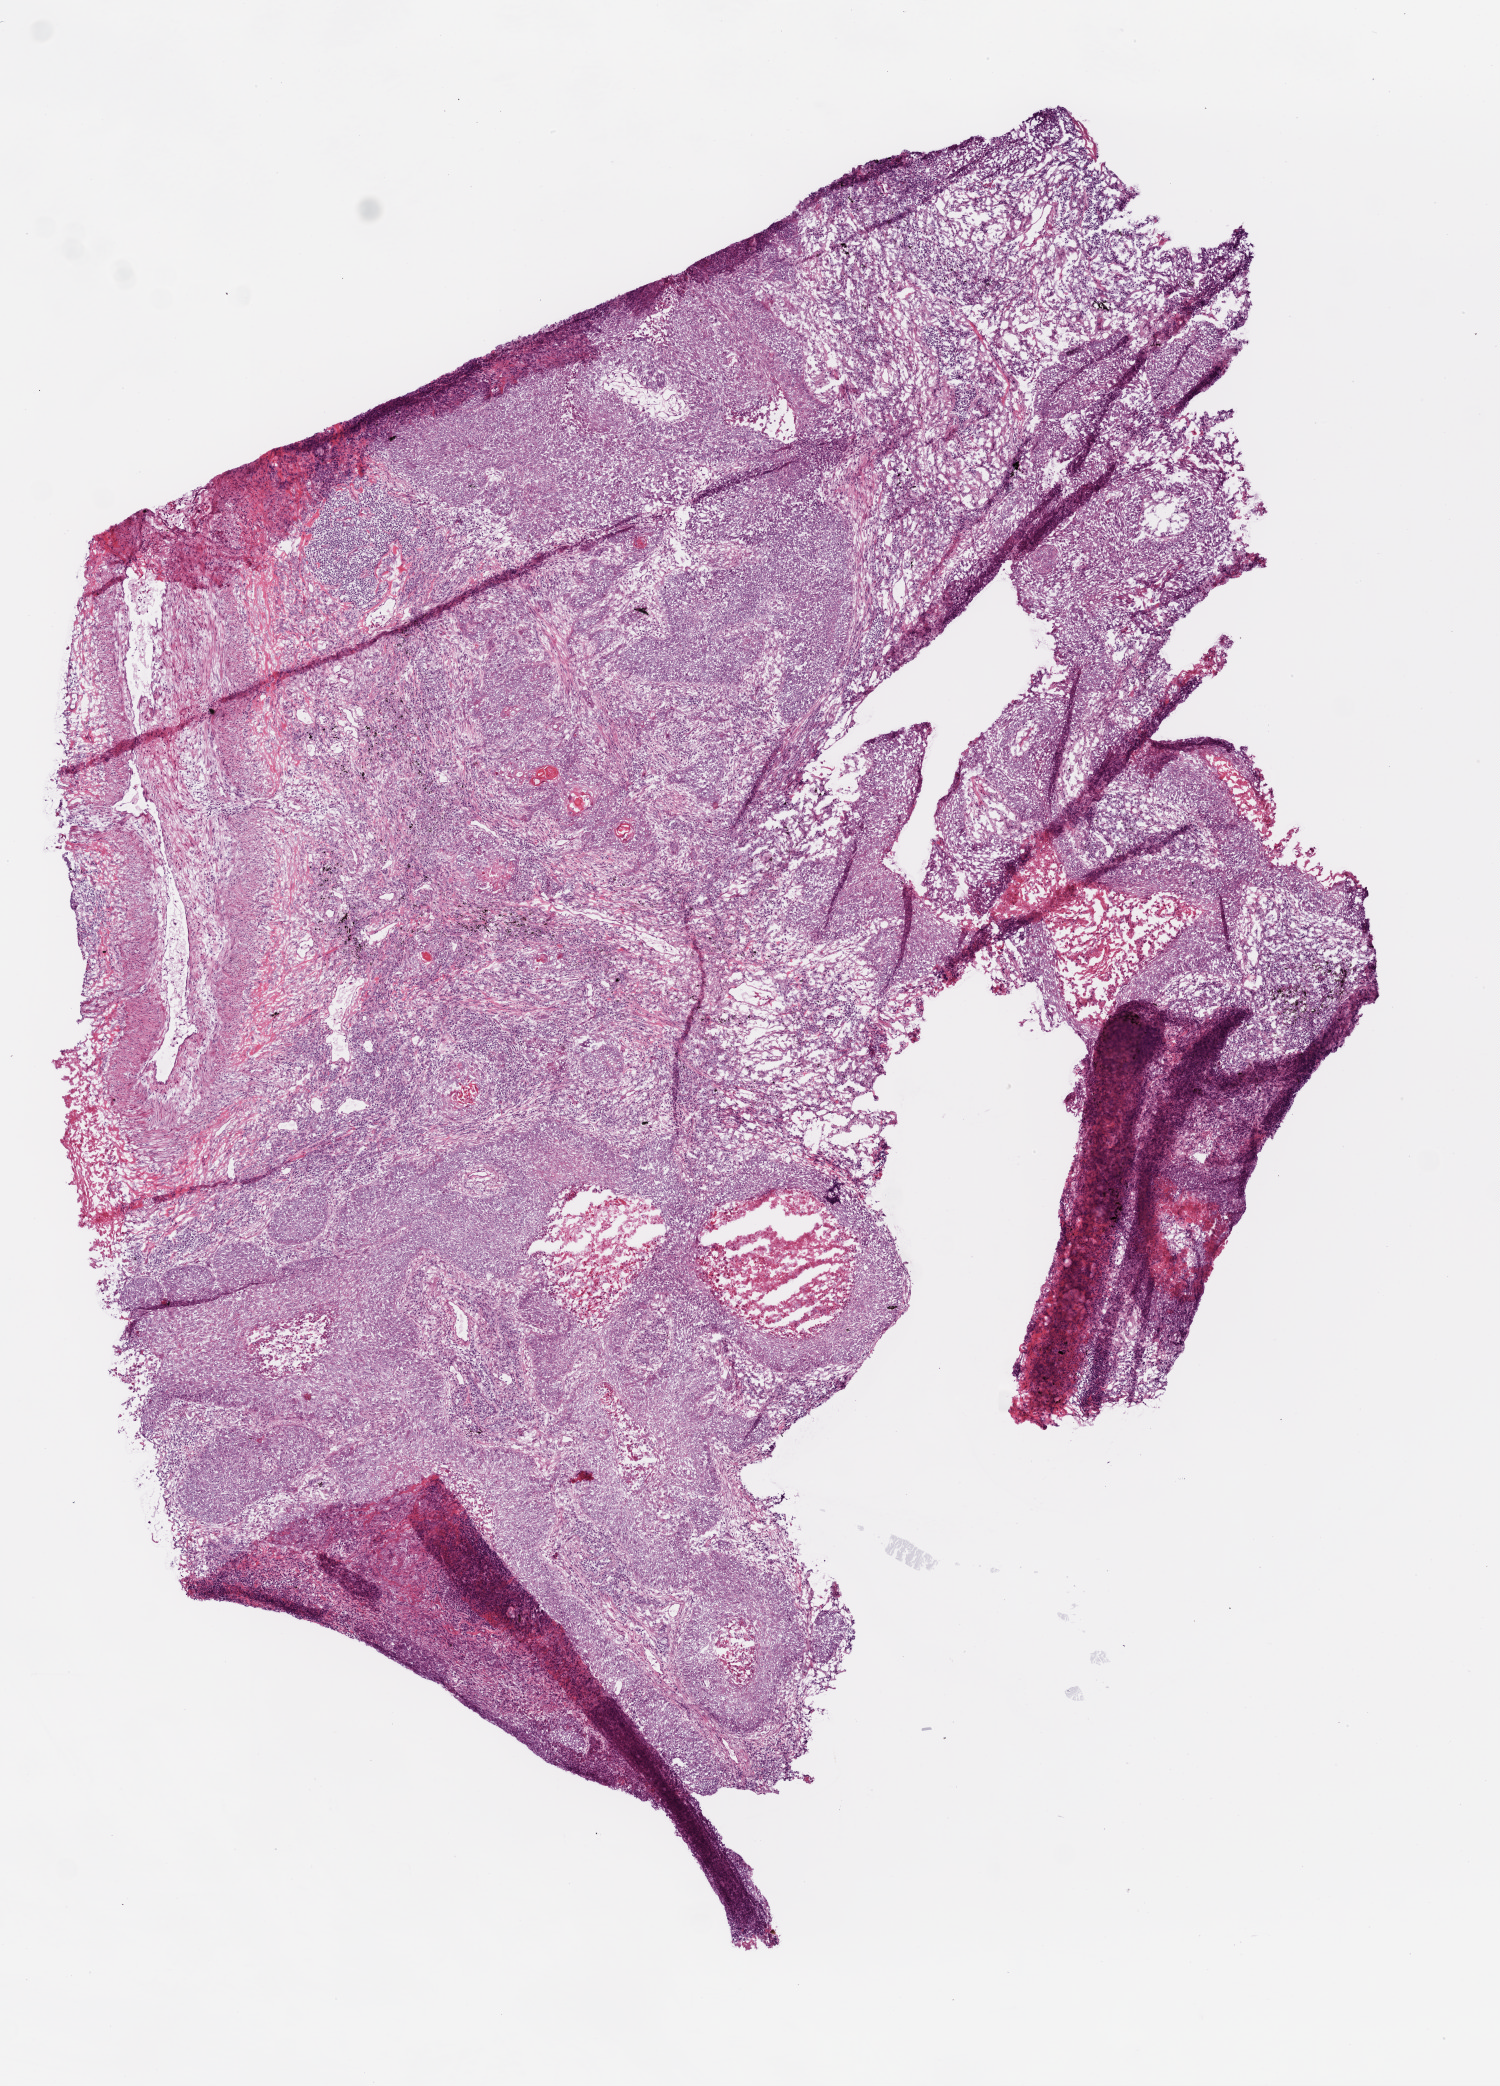
Digitized H&E-stained tissue section (whole slide) — shown as a low-resolution overview of the whole scanned area (about 6.0 x 8.4 mm, slide scanned at 20x). Frozen section. Sample: primary tumour, lung. Patient: male, age at initial diagnosis 64 years. Slide review estimates, as recorded: tumour cells 80%, tumour nuclei 80%, normal cells 0%, stromal cells 15%, necrosis 5%.
AJCC pathologic stage: IB. Histologic diagnosis: Squamous cell carcinoma, NOS (lower lobe, lung).